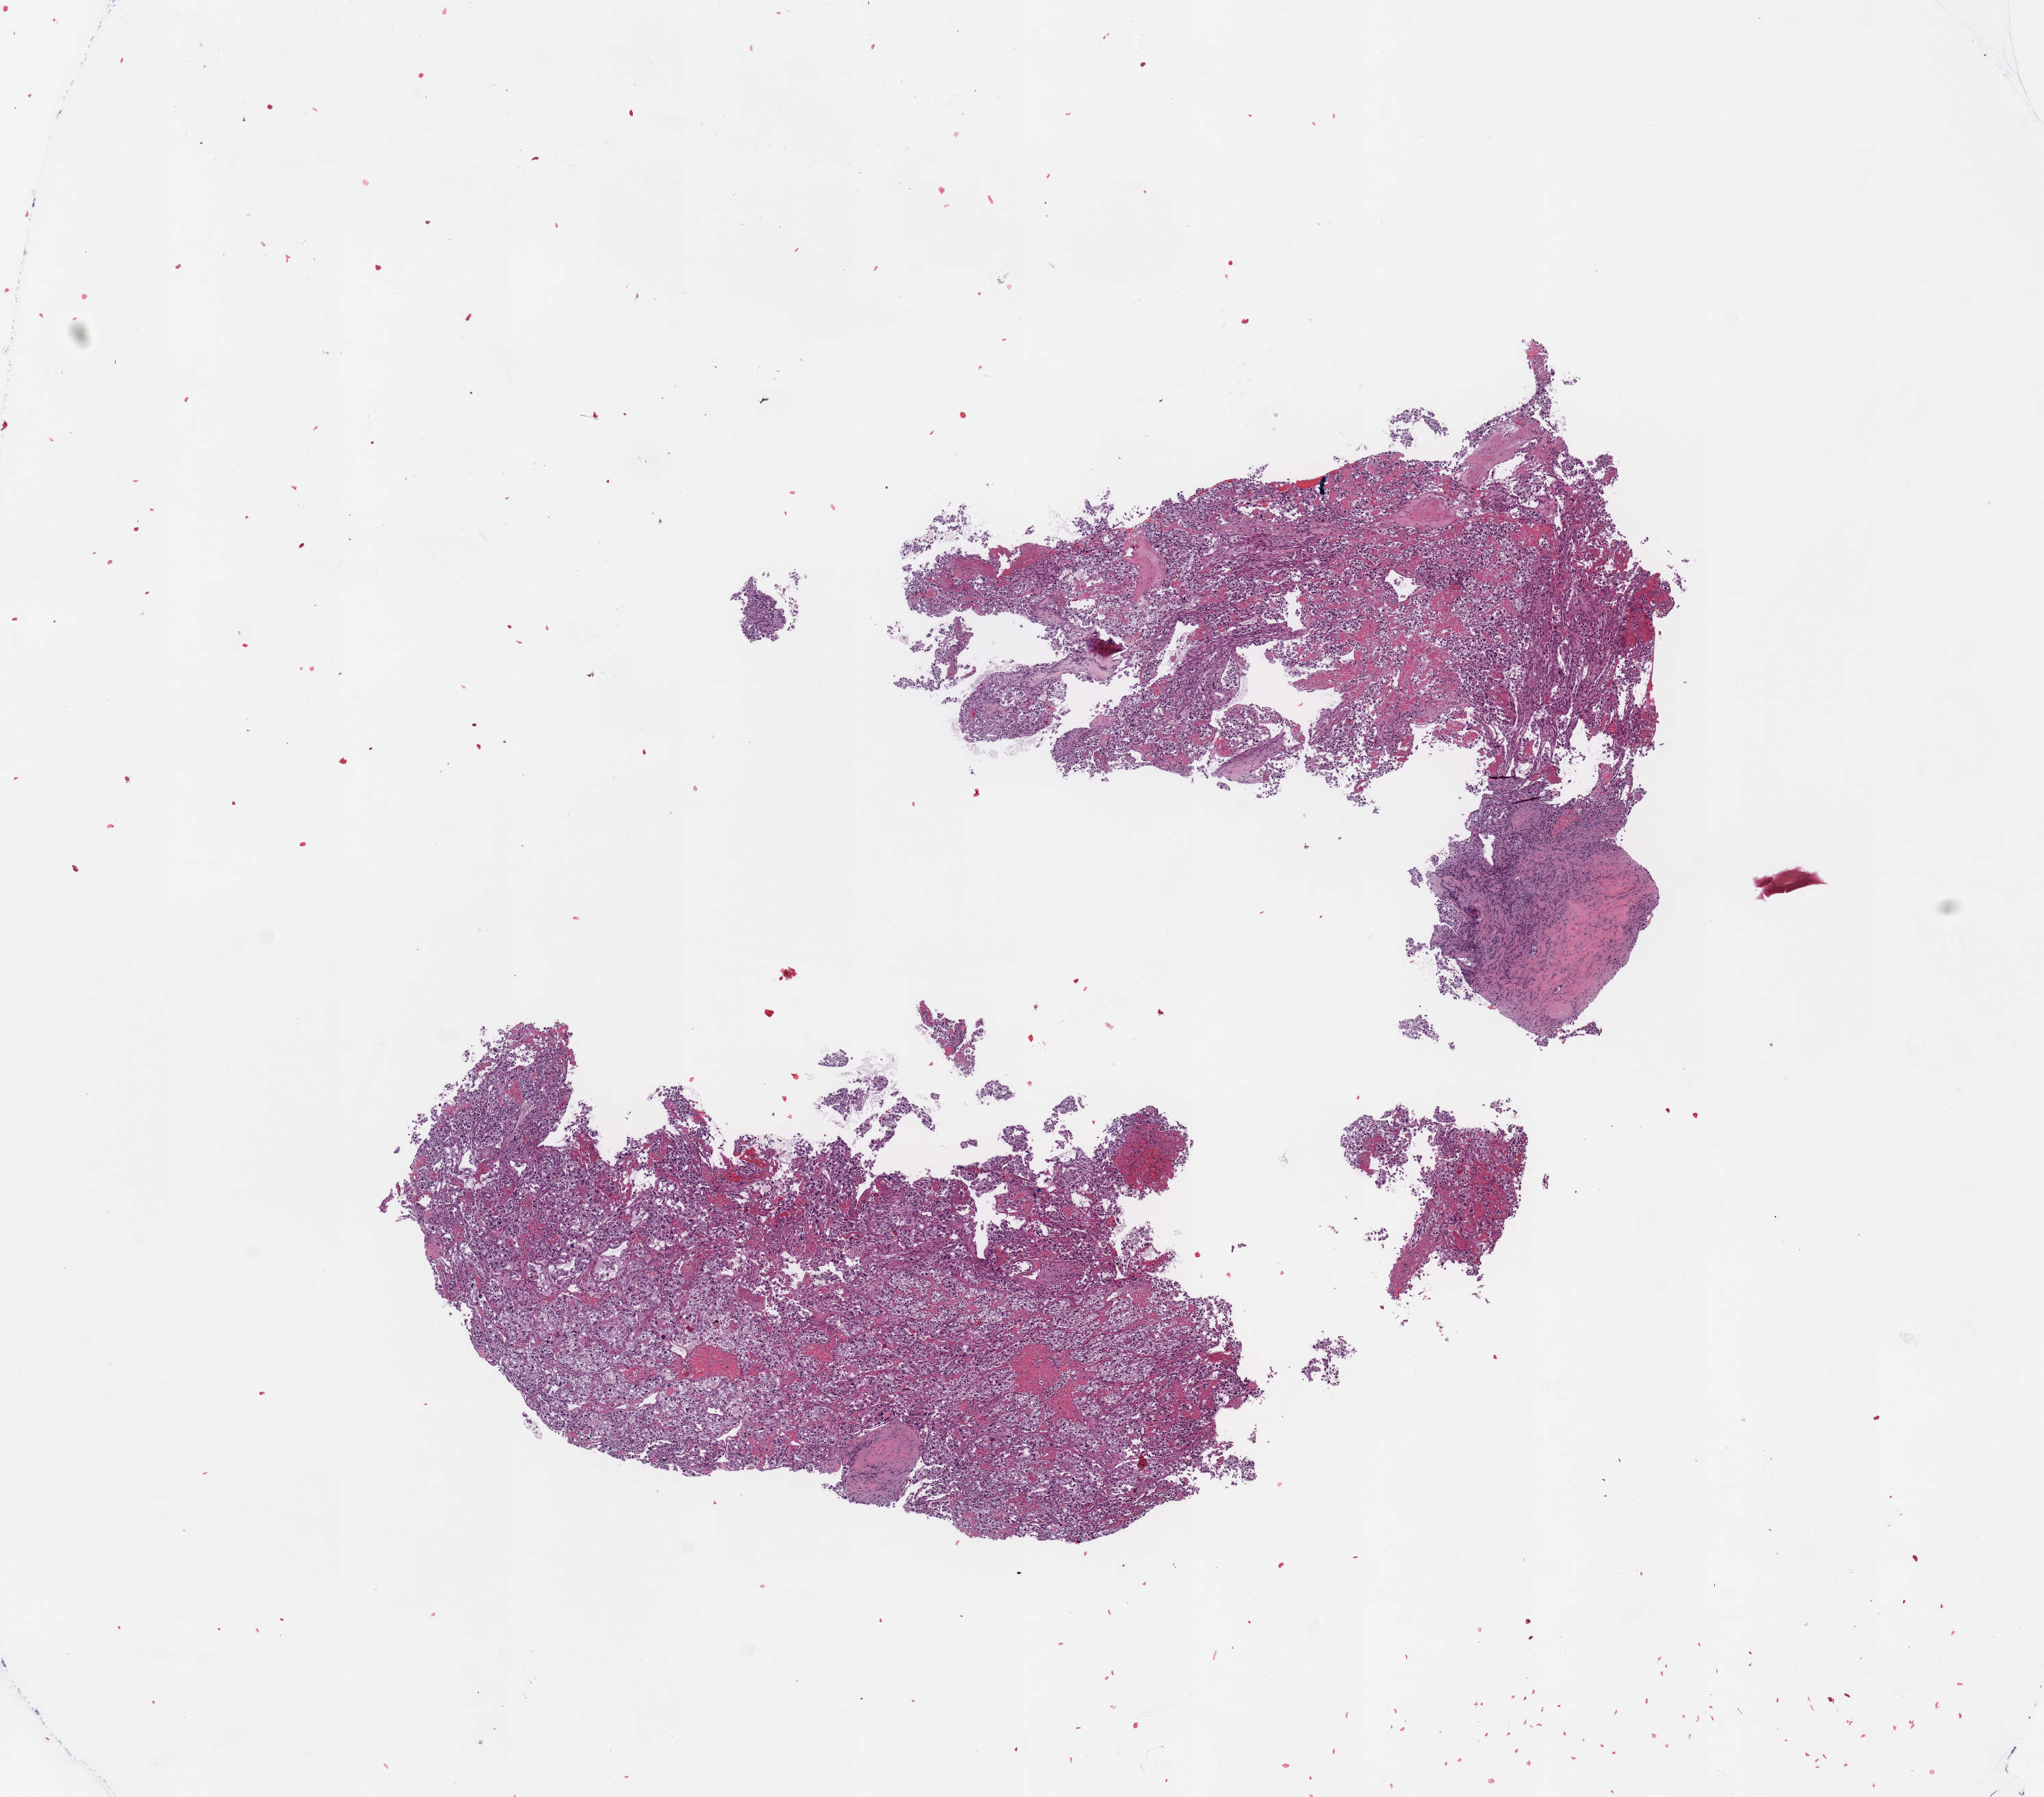
Whole-slide histology image, H&E-stained, a low-resolution overview of the entire scanned area, about 11.8 x 10.4 mm (slide scanned at 20x). Kidney, tumour tissue. Male, 47 y/o. Histologic grade: G4 (undifferentiated).
- primary tumour site (as recorded): lower pole
- histologic diagnosis: Renal cell carcinoma, NOS
- AJCC pathologic stage: III